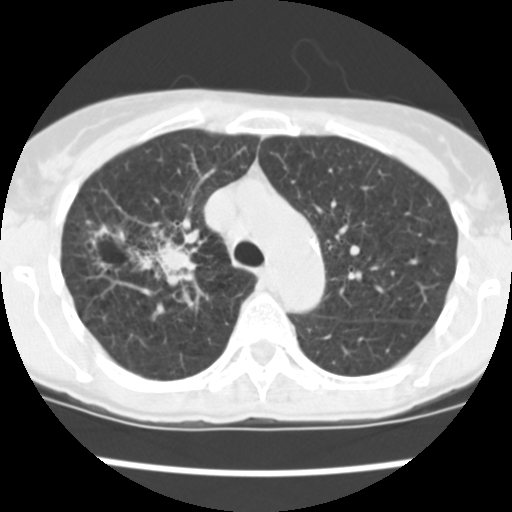
Low-dose screening chest CT, one axial slice; slice 177 of 252 in the series (ordered by position); lung window (W 1500 / L -600 HU); 2.5 mm slice thickness; 512 × 512 image matrix, field of view 276 × 276 mm.
Annotated regions visible in this slice (manually delineated by an expert):
- lesion 2 (tumor, lower lobe of right lung): bounding box <133,241,196,284> (left, top, right, bottom; pixels)